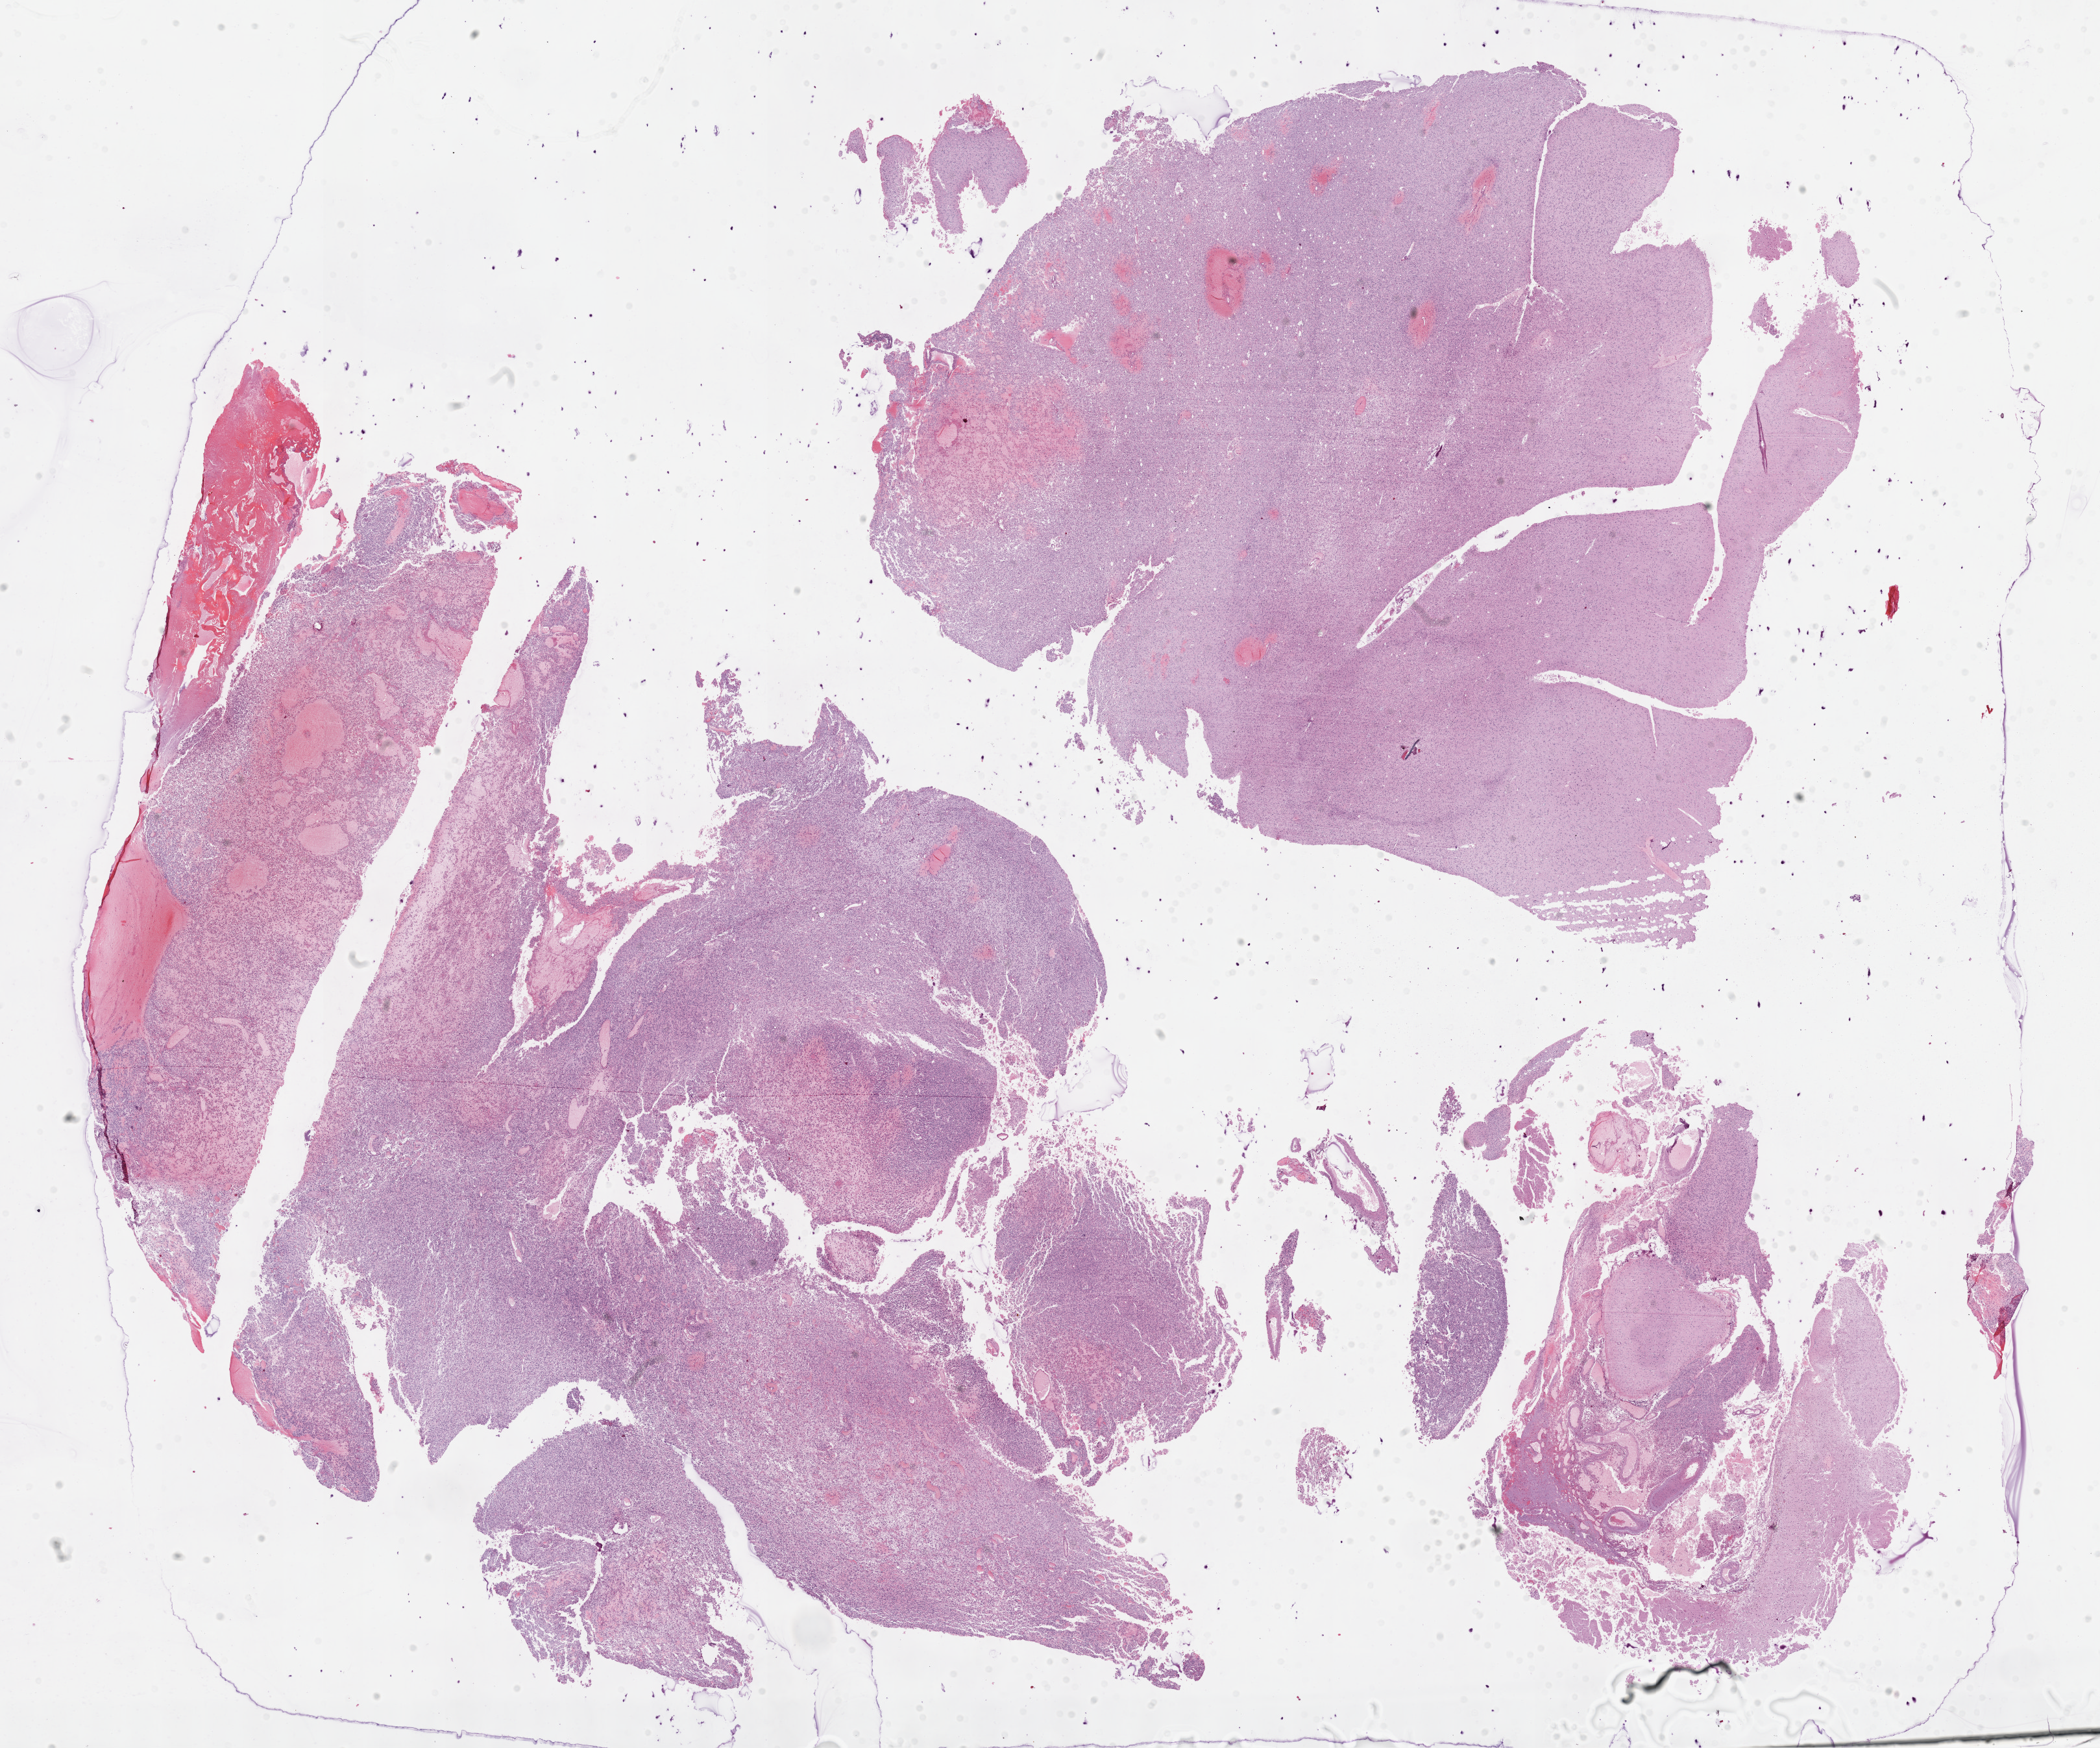
Hematoxylin and eosin (H&E) stained whole-slide image — low-resolution overview of the scanned area, about 26.2 x 21.8 mm. Formalin-fixed paraffin-embedded (FFPE) diagnostic section. Primary tumour sample from the brain. Female patient; age at initial diagnosis 28 years. Histologic grade: G3 (poorly differentiated).
Laterality: right. Histologic diagnosis: Mixed glioma (cerebrum).